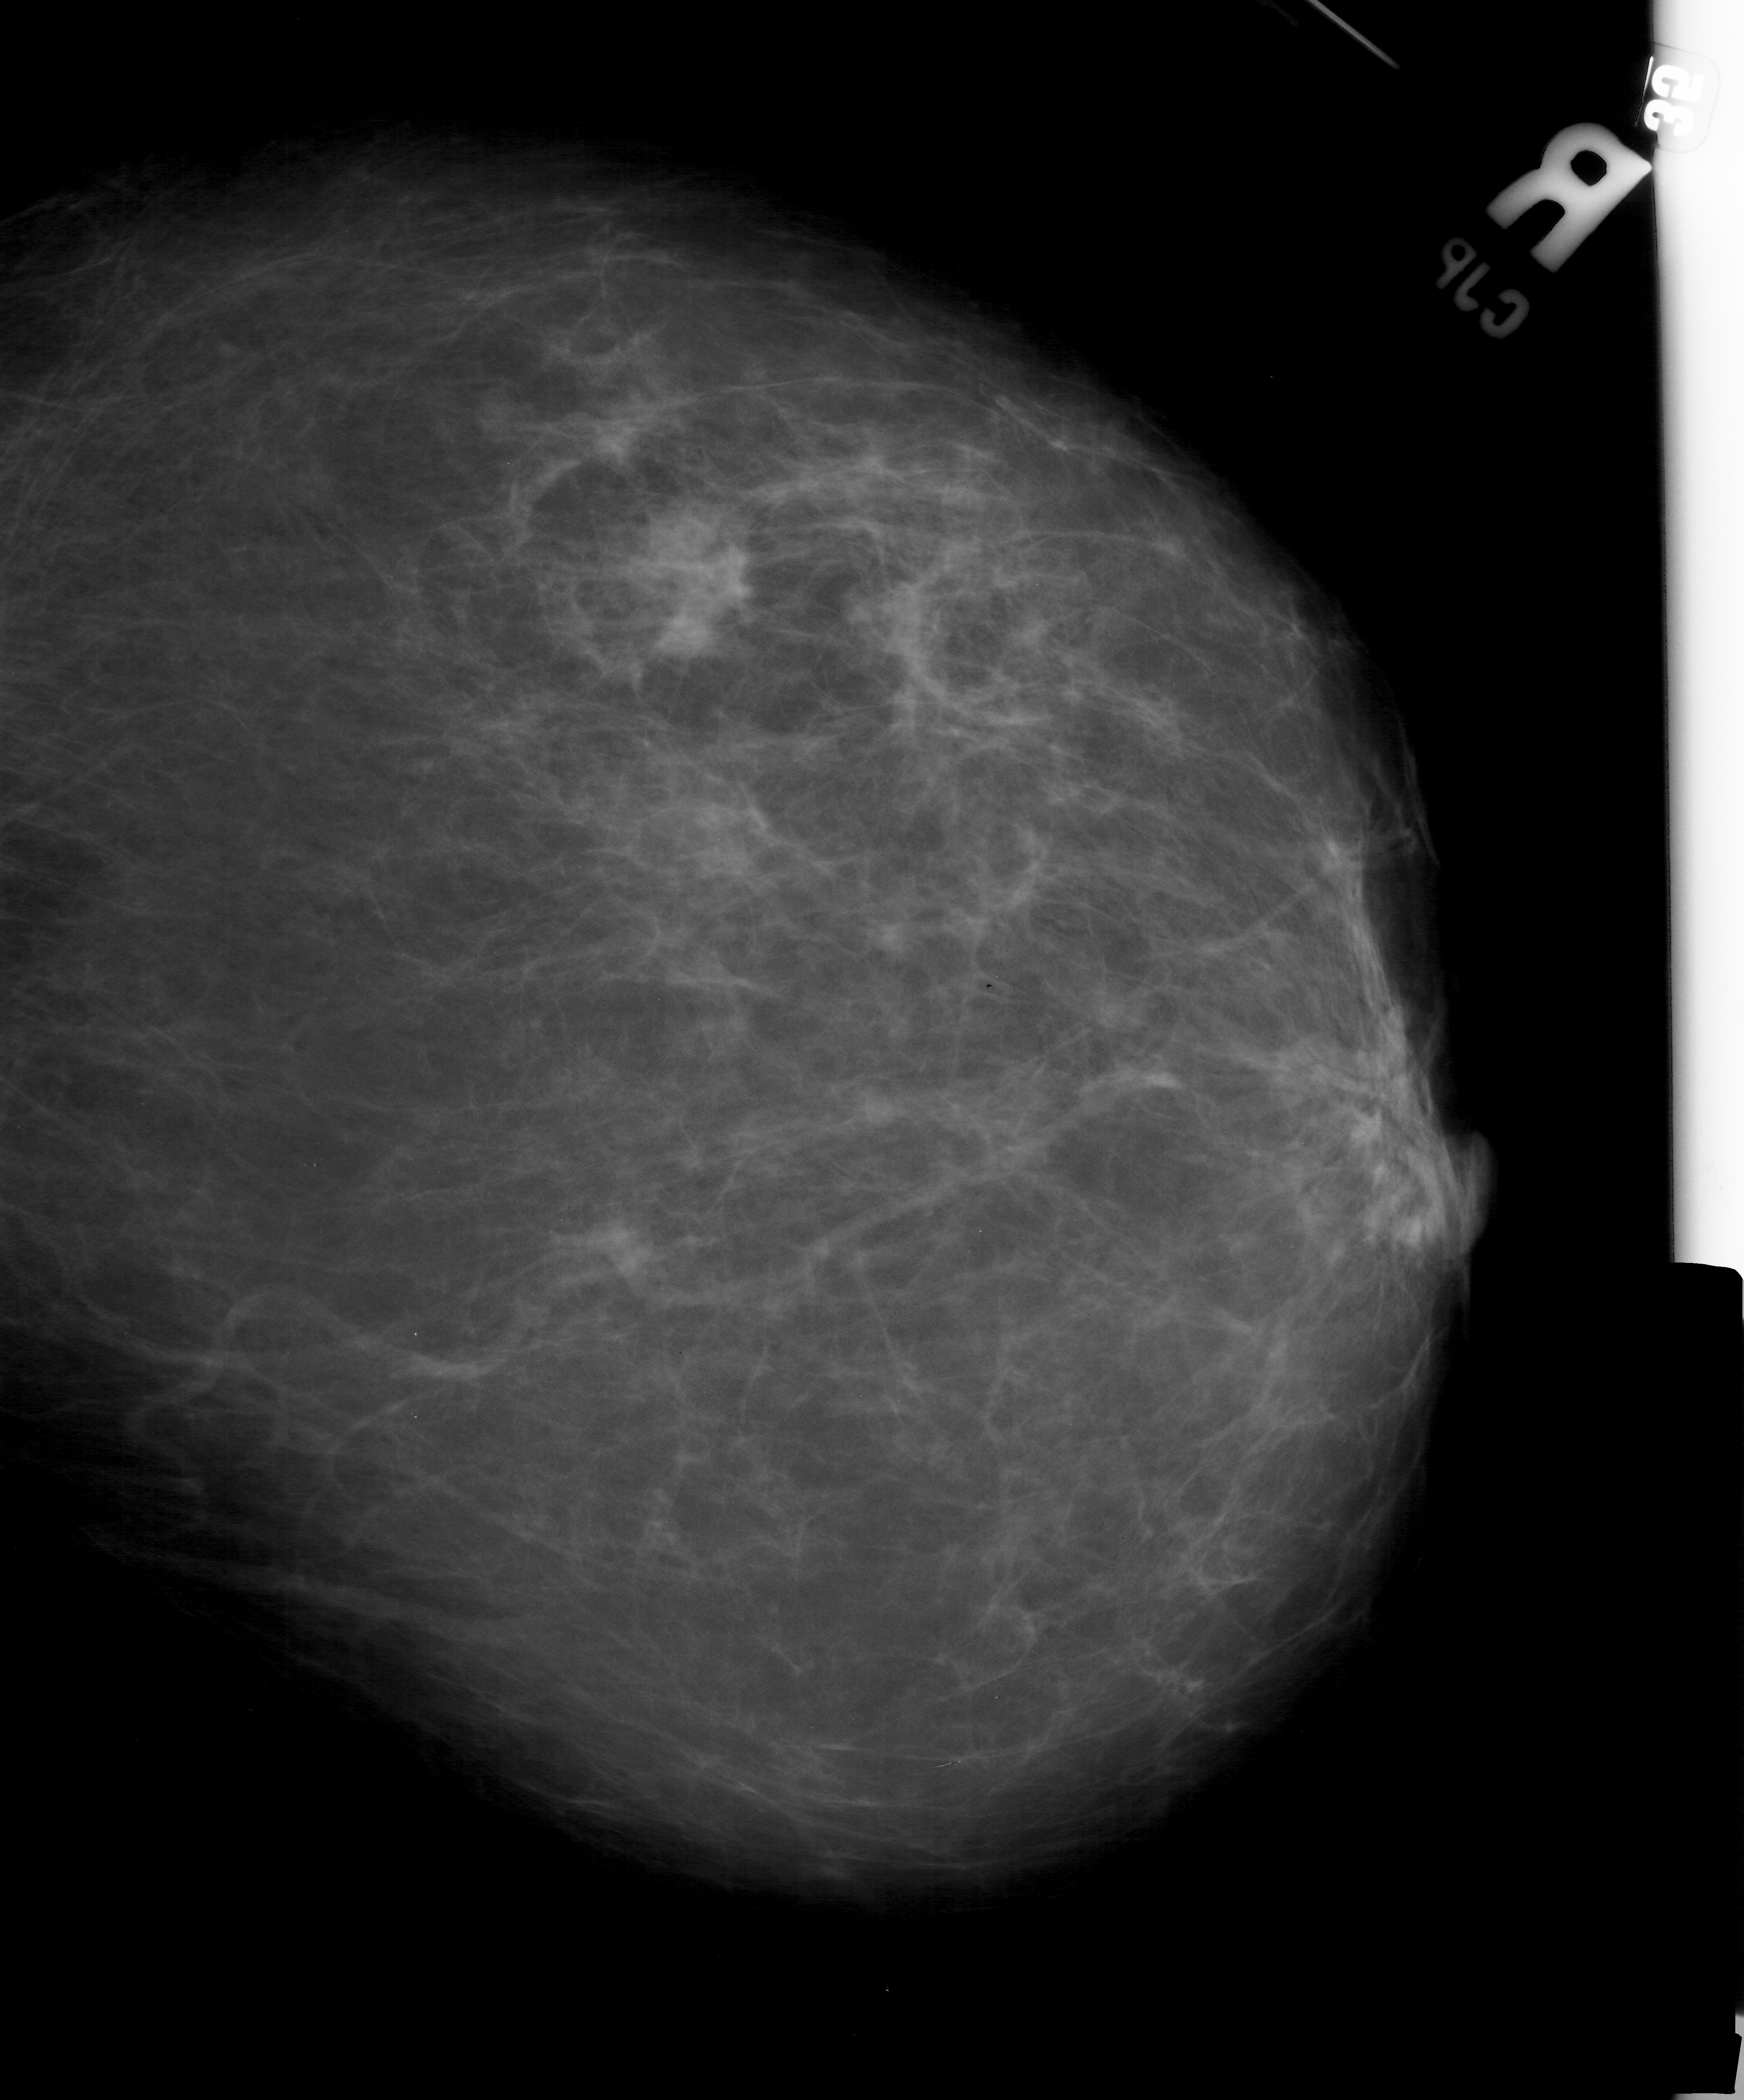
Digitized screen-film mammogram, right breast, CC view, breast composition: scattered fibroglandular densities (BI-RADS density category 2 of 4).
Marked abnormality: mass, shape irregular, margins ill defined; BI-RADS assessment category 4; pathology result (as recorded, not read from the image): malignant.